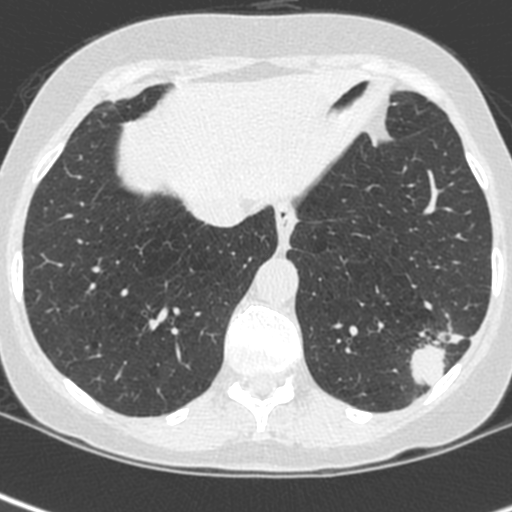
Chest CT (low-dose screening protocol), one axial image; baseline screening round; lung window (W 1500 / L -600 HU); standard (soft-tissue) reconstruction kernel (C); 120 kVp; slice 181 of 252 in the series. Female participant, aged 56 years at enrolment. Current smoker at enrolment.
Expert-annotated lung lesion, bounding box [x1, y1, x2, y2] px = [400, 305, 480, 387]. Screening reader's record for this exam (one nodule recorded; not confirmed to be the boxed lesion): non-calcified nodule or mass ≥4 mm, left lower lobe, 37 × 29 mm, spiculated (stellate) margins, ground glass attenuation. Official screen result: positive, change unspecified: nodule(s) >= 4 mm or enlarging nodule(s), mass(es), or other non-specific abnormalities suspicious for lung cancer. Later outcome: lung cancer diagnosed 91 days after this screen — squamous cell carcinoma, NOS, left lower lobe, poorly differentiated (G3), stage IIIA (AJCC 6th edition), 35 mm at pathology.